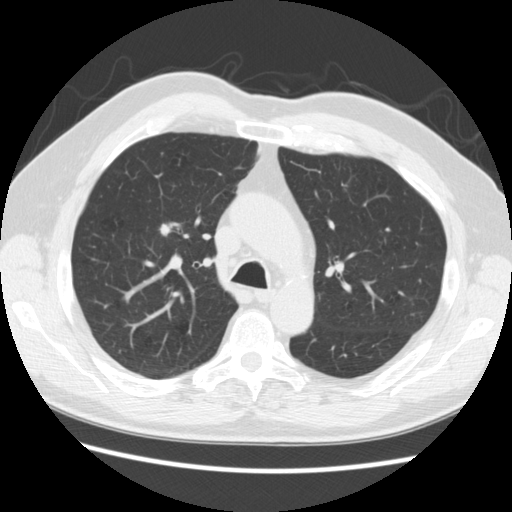
Low-dose screening chest CT, axial slice; baseline annual screen; lung window (W 1500 / L -600 HU); slice 83 of 259 in the series. Male participant, aged 69 years at enrolment. Former smoker at enrolment.
Expert reader's lesion annotation, bounding box [x1, y1, x2, y2] px = [150, 216, 191, 247]. The exam's reader record, not a measurement of the box and not confirmed to be the same lesion: non-calcified nodule or mass ≥4 mm, right upper lobe, 9 × 7 mm, poorly defined margins, soft tissue attenuation. Later outcome: lung cancer diagnosed 50 days after this screen — adenocarcinoma, NOS, right upper lobe, moderately differentiated (G2), stage IA (AJCC 6th edition), 9 mm at pathology.